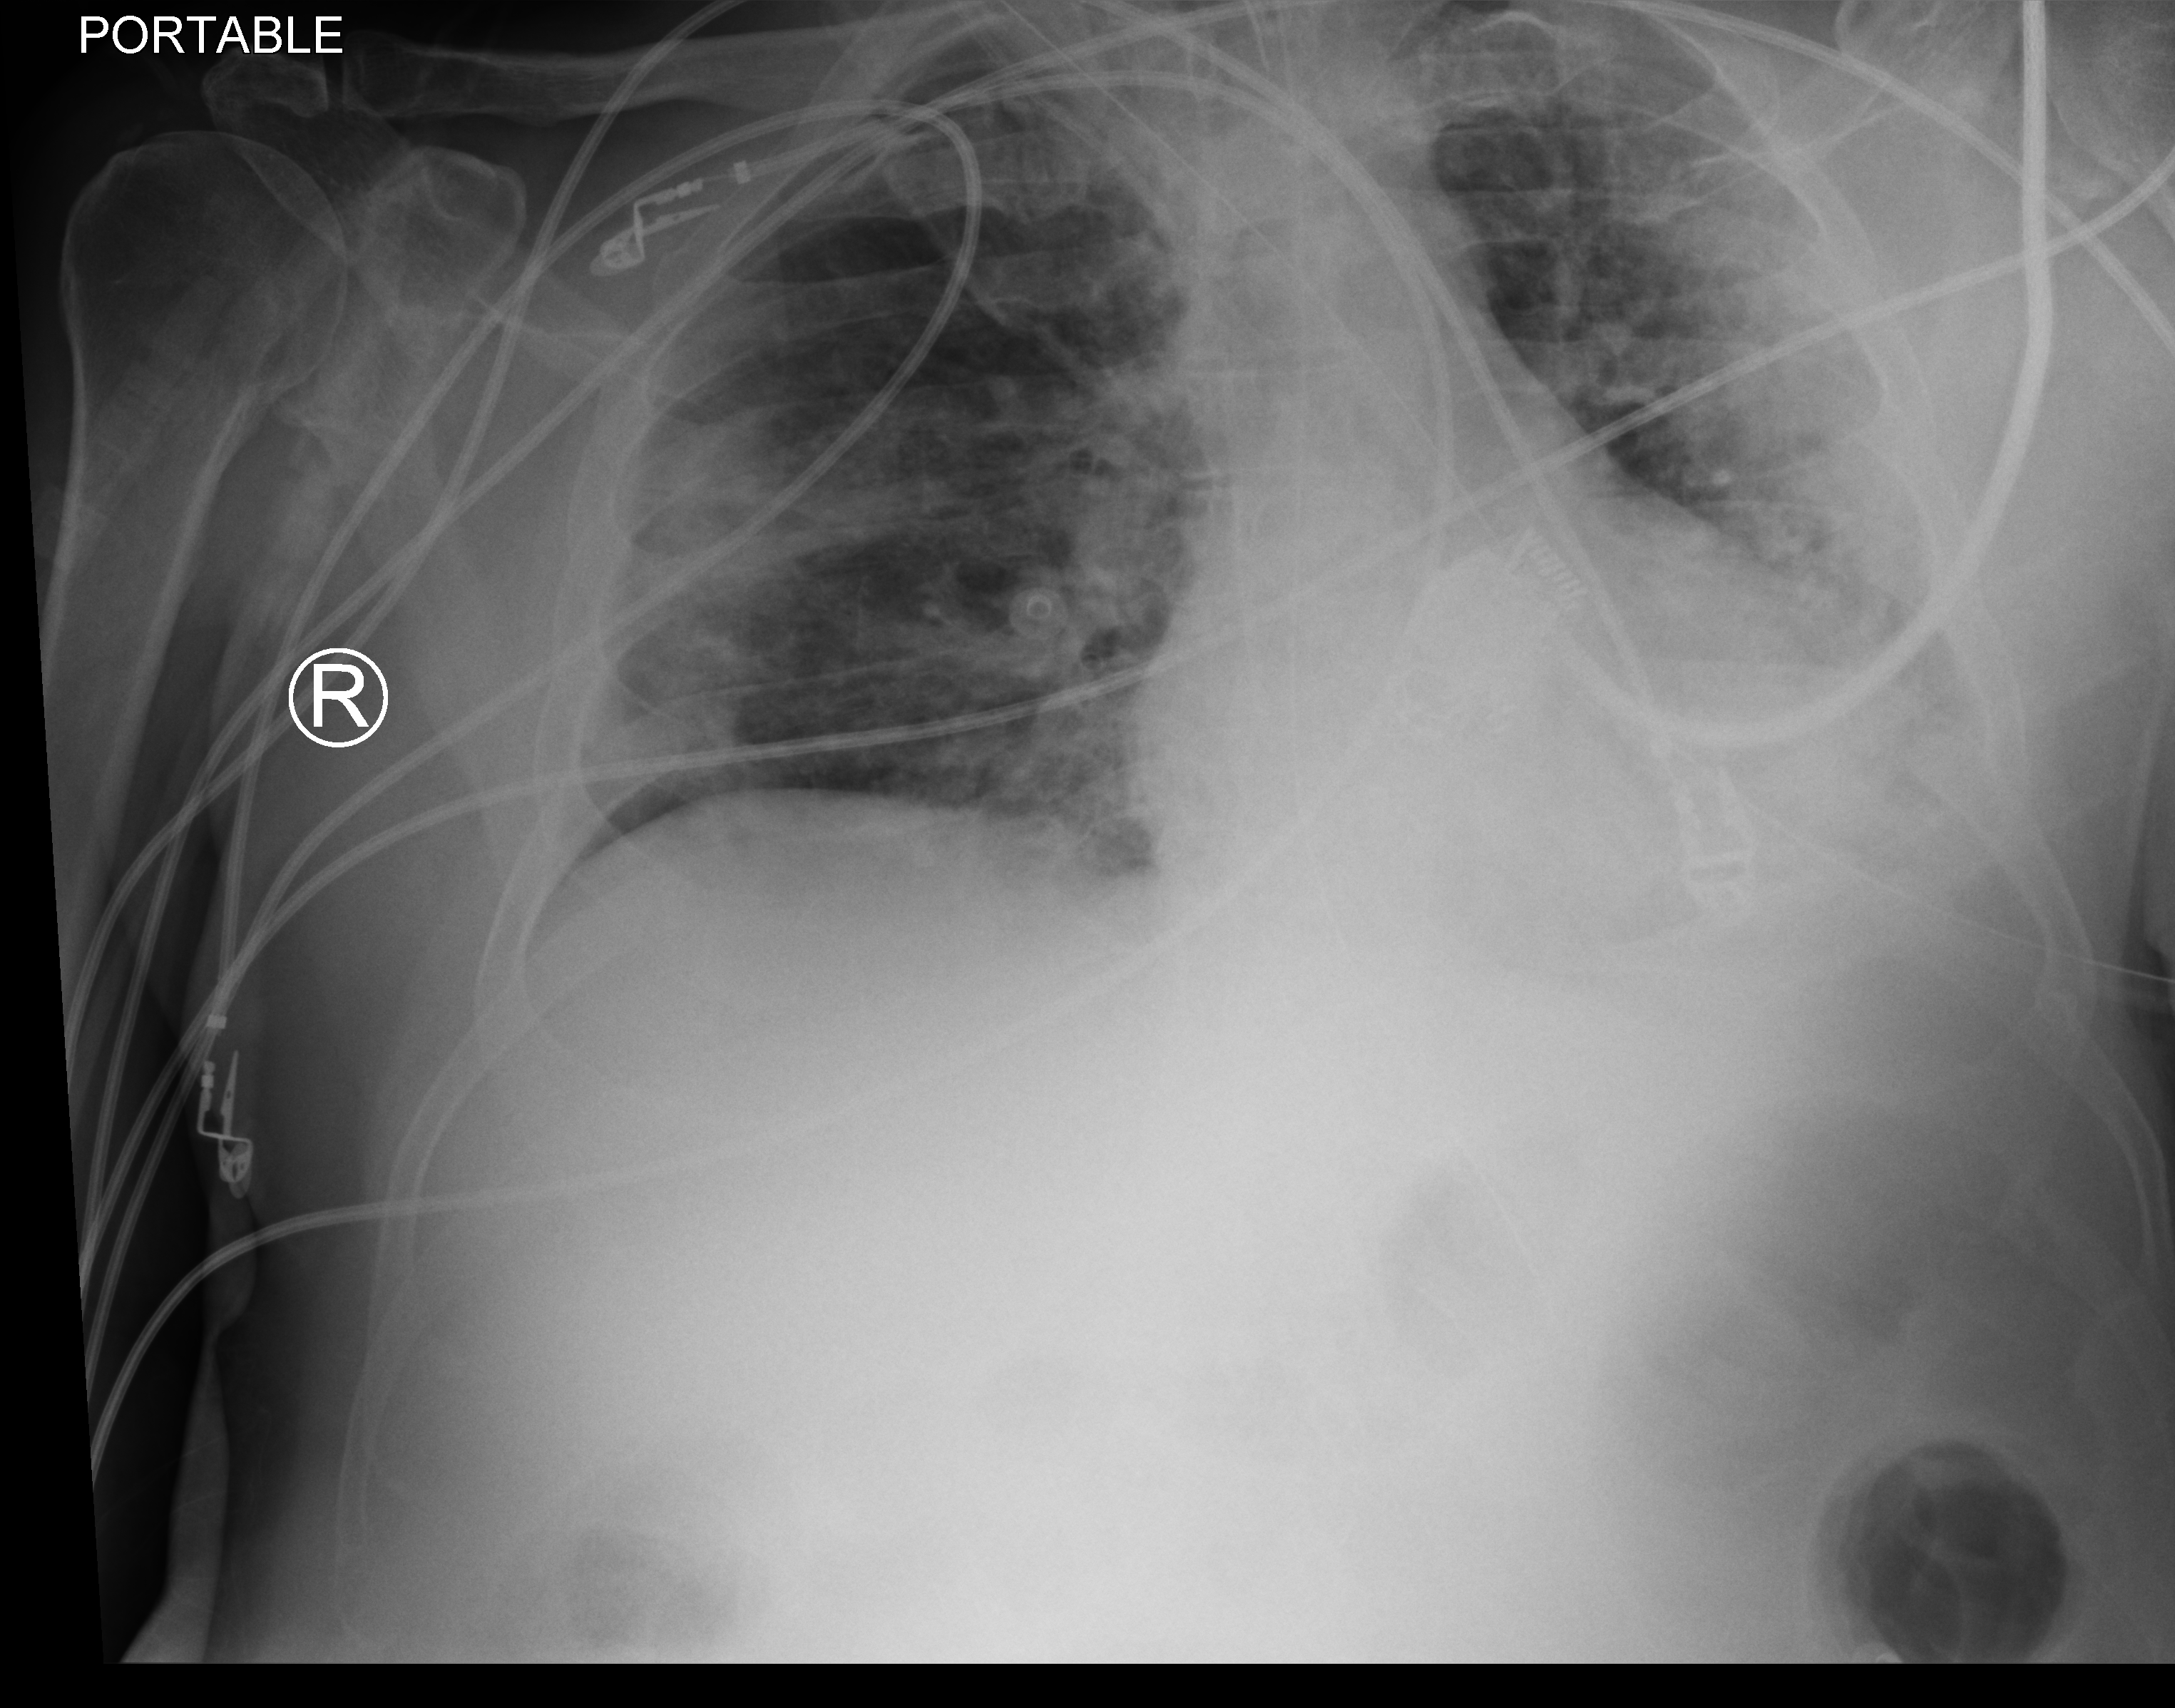
Bedside chest radiograph (computed radiography); anteroposterior (AP) projection. Male patient hospitalised with COVID-19, age 18–59 years.
Admission-level facts for this patient (not findings on this image; timing relative to this image not recorded): length of hospital stay: 25 days; mechanically ventilated during this hospital stay: yes; admitted to intensive care during this hospital stay: yes.